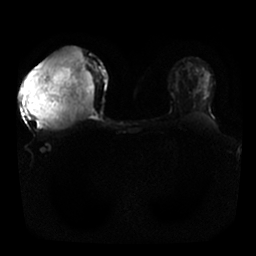
Breast MRI, one axial slice; position 15 of 25 along the scan axis; diffusion-weighted series; image 2 of 4 stored at this slice position (different b-values; order by instance number); 1.5 T; 4 mm slice thickness; 256 × 256 image matrix. Female patient.
Annotated regions visible in this slice (outlined manually by an expert reader):
- tumour on diffusion-weighted imaging: bounding box [x1, y1, x2, y2] px = [20, 48, 95, 130]